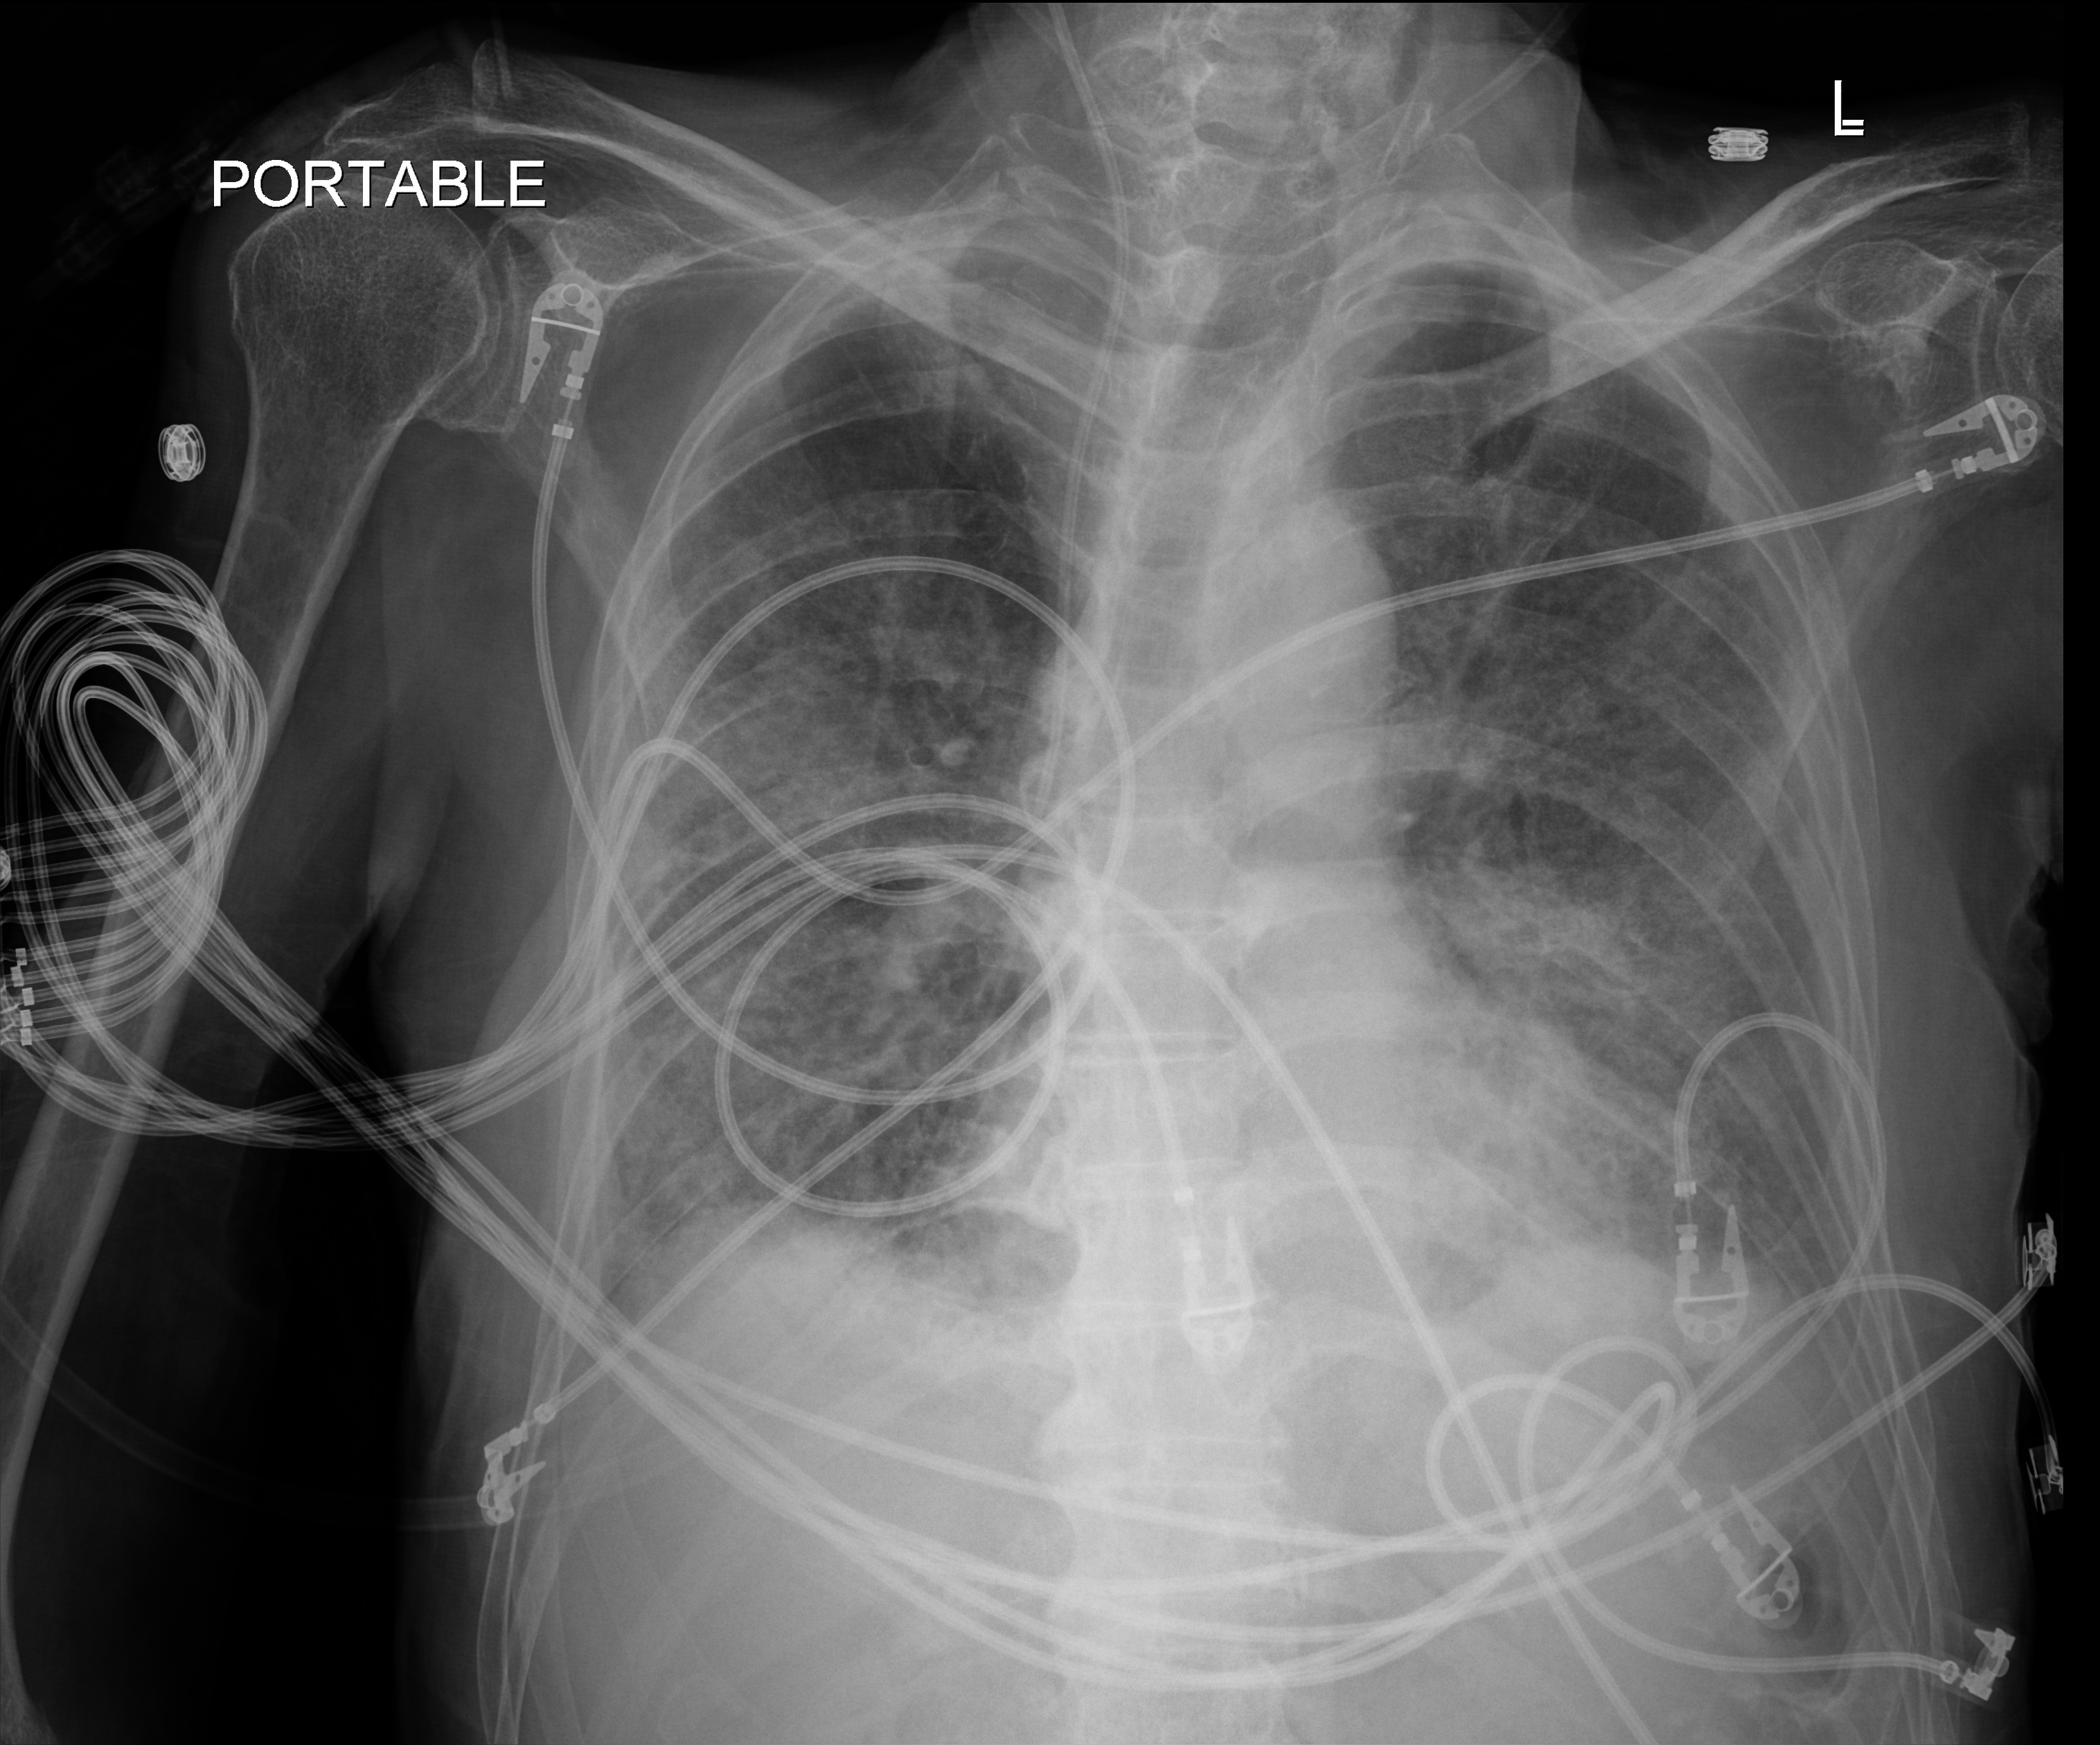
Chest X-ray (portable), anteroposterior (AP) projection. Male patient hospitalised with COVID-19, age 60–74 years.
From the hospital-stay record, not from the radiograph (when in the stay this image was taken is not recorded): hypertension (admission record): yes; mechanically ventilated during this hospital stay: yes; length of hospital stay: 42 days.